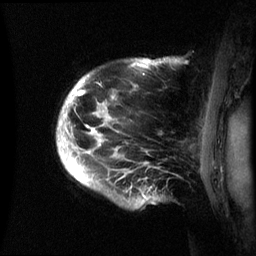
Breast MRI (dynamic contrast-enhanced), one sagittal slice; position 51 of 60 along the scan axis; dynamic contrast-enhanced series, image 2 of 3 at this slice position (ordered by acquisition); 1.5 T; TE 4.2 ms, TR 8.4 ms; 2.4 mm slice thickness; 256 × 256 image matrix, field of view 230 × 230 mm. Patient: female, 48 years.
Annotated regions visible in this slice (semi-automatic segmentation, software-assisted and operator-edited):
- analysis volume of interest (the breast-tissue region the enhancement analysis was run in; not a lesion): box from (x=57, y=58) to (x=180, y=208) px
- tumour enhancement mask (voxels above the 70 % enhancement threshold inside the analysis volume of interest): (x=59, y=60)–(x=150, y=198)